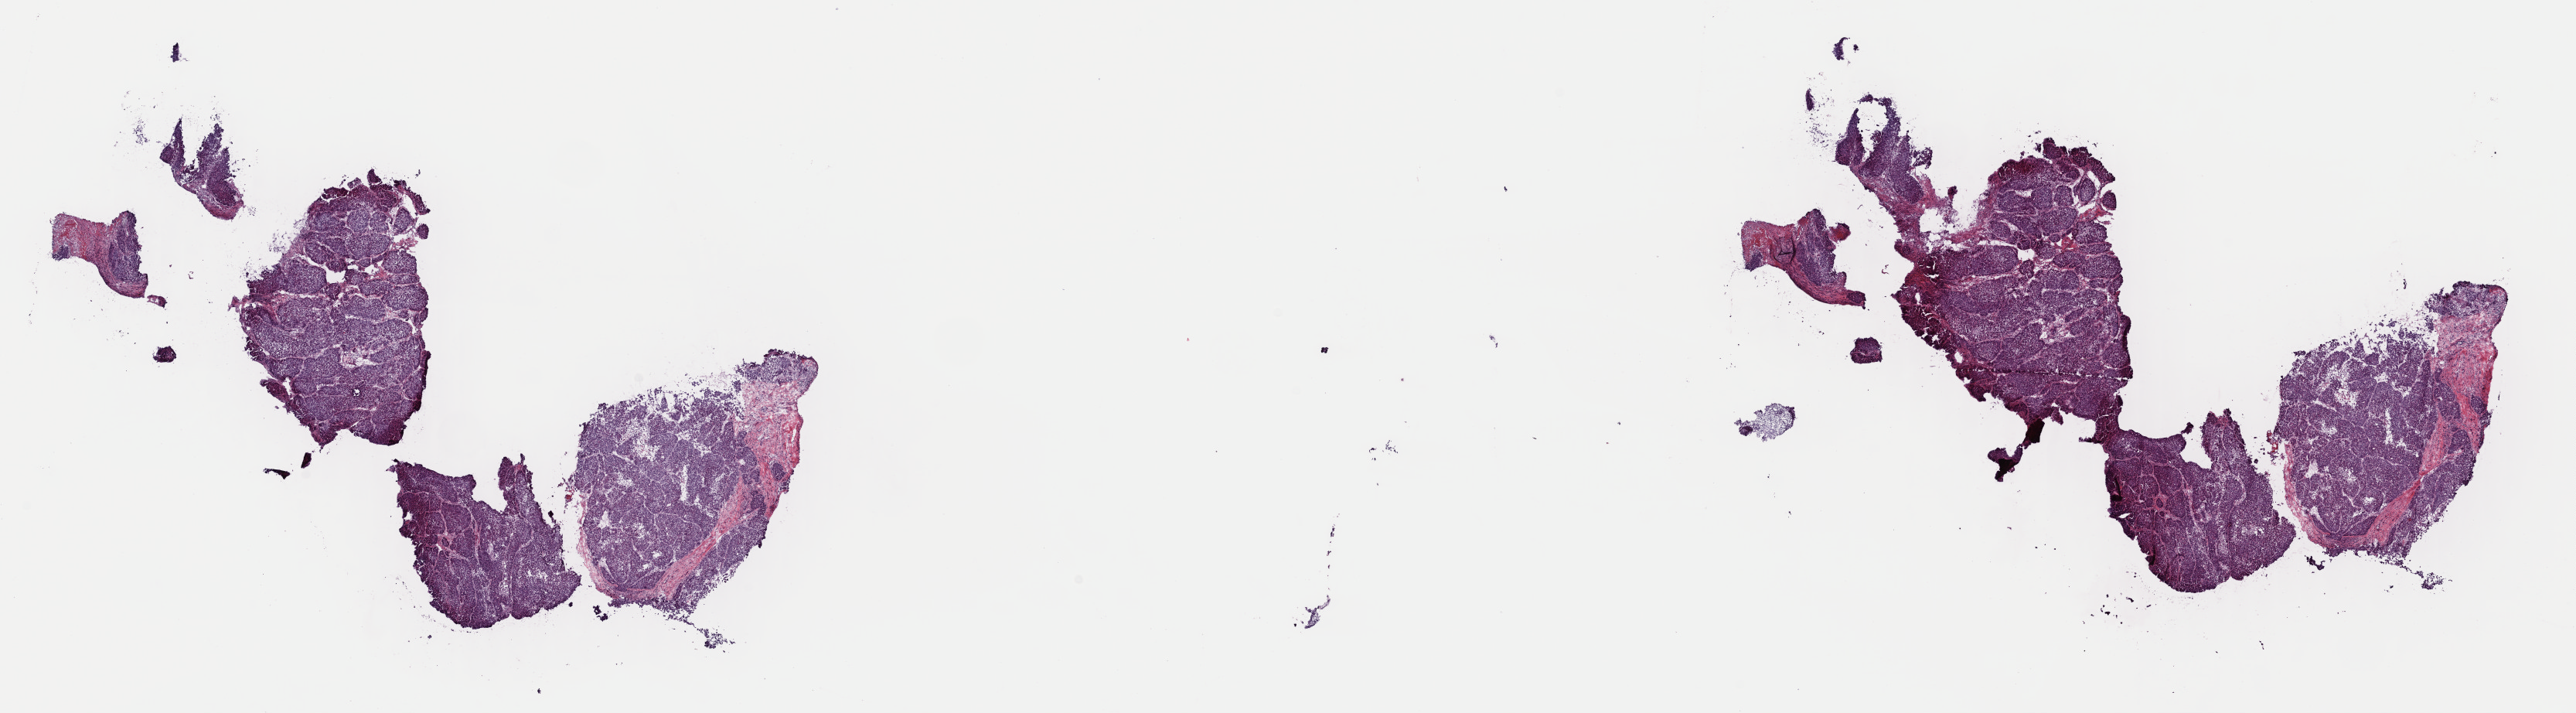
Whole-slide histology image, H&E-stained — whole scanned area (about 26.3 x 7.3 mm) shown as a low-resolution overview, frozen section from the top of the tissue portion, primary tumour sample from the liver. Male patient; age at initial diagnosis 64 years. Histologic grade: G3 (poorly differentiated). Composition of this section per pathologist review: tumour cells 85%, tumour nuclei 85%, normal cells 0%, stromal cells 14%, necrosis 1%. Inflammatory infiltration, as recorded: lymphocyte infiltration 2%, monocyte infiltration 1%, neutrophil infiltration 1%.
• AJCC pathologic stage: II
• diagnosis: Hepatocellular carcinoma, NOS